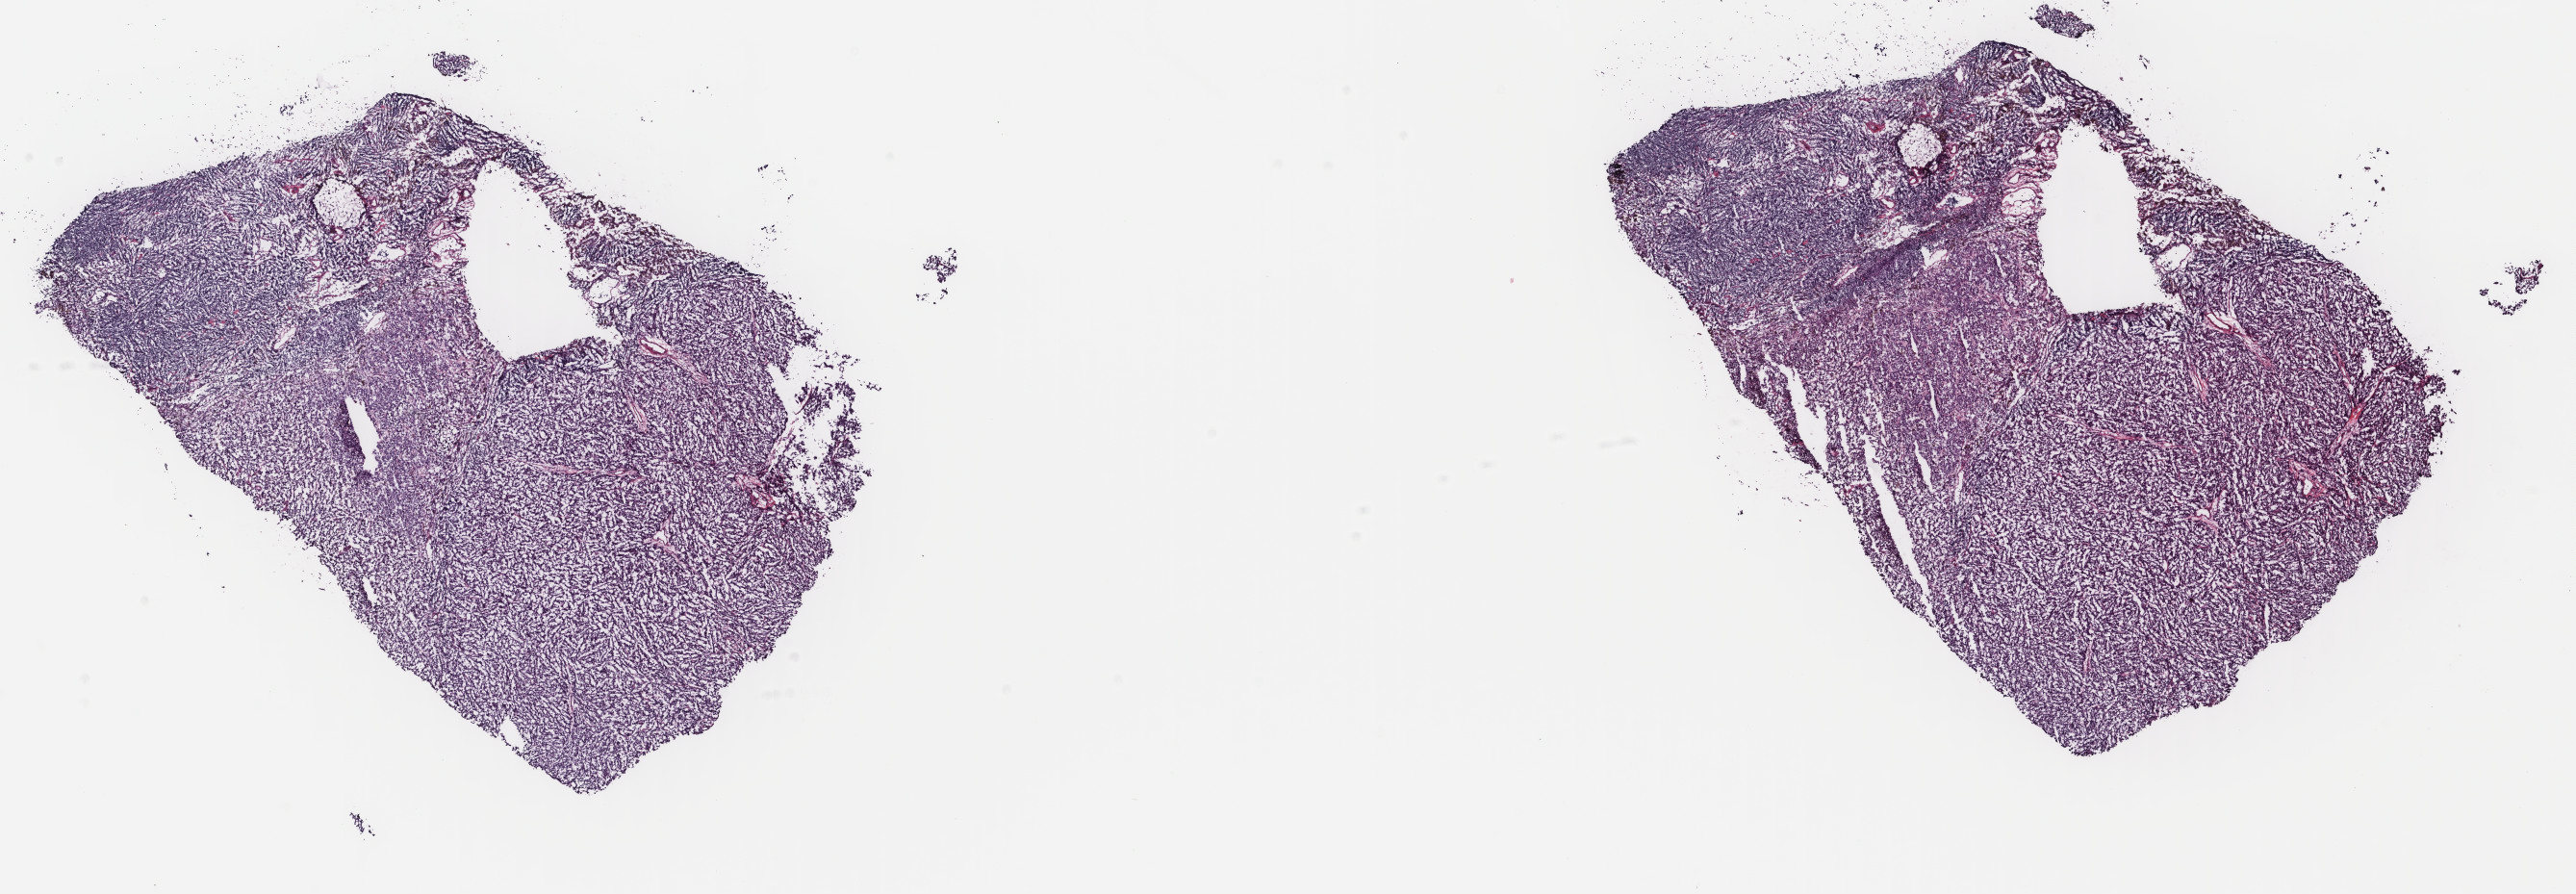
Whole-slide histology image, H&E-stained, low-resolution overview of the scanned area, about 21.2 x 7.4 mm (from a 40x scan); frozen section from the top of the tissue portion; metastatic tumour sample, sampled site: lymph nodes of axilla or arm. Male patient; age at initial diagnosis 77 years. Composition of this section per pathologist review: tumour cells 100%, tumour nuclei 95%, normal cells 0%, stromal cells 0%, necrosis 0%. Inflammatory infiltration, as recorded: lymphocyte infiltration 0%, monocyte infiltration 0%, neutrophil infiltration 0%.
This section: metastatic tumour tissue. Patient diagnosis: Malignant melanoma, NOS.